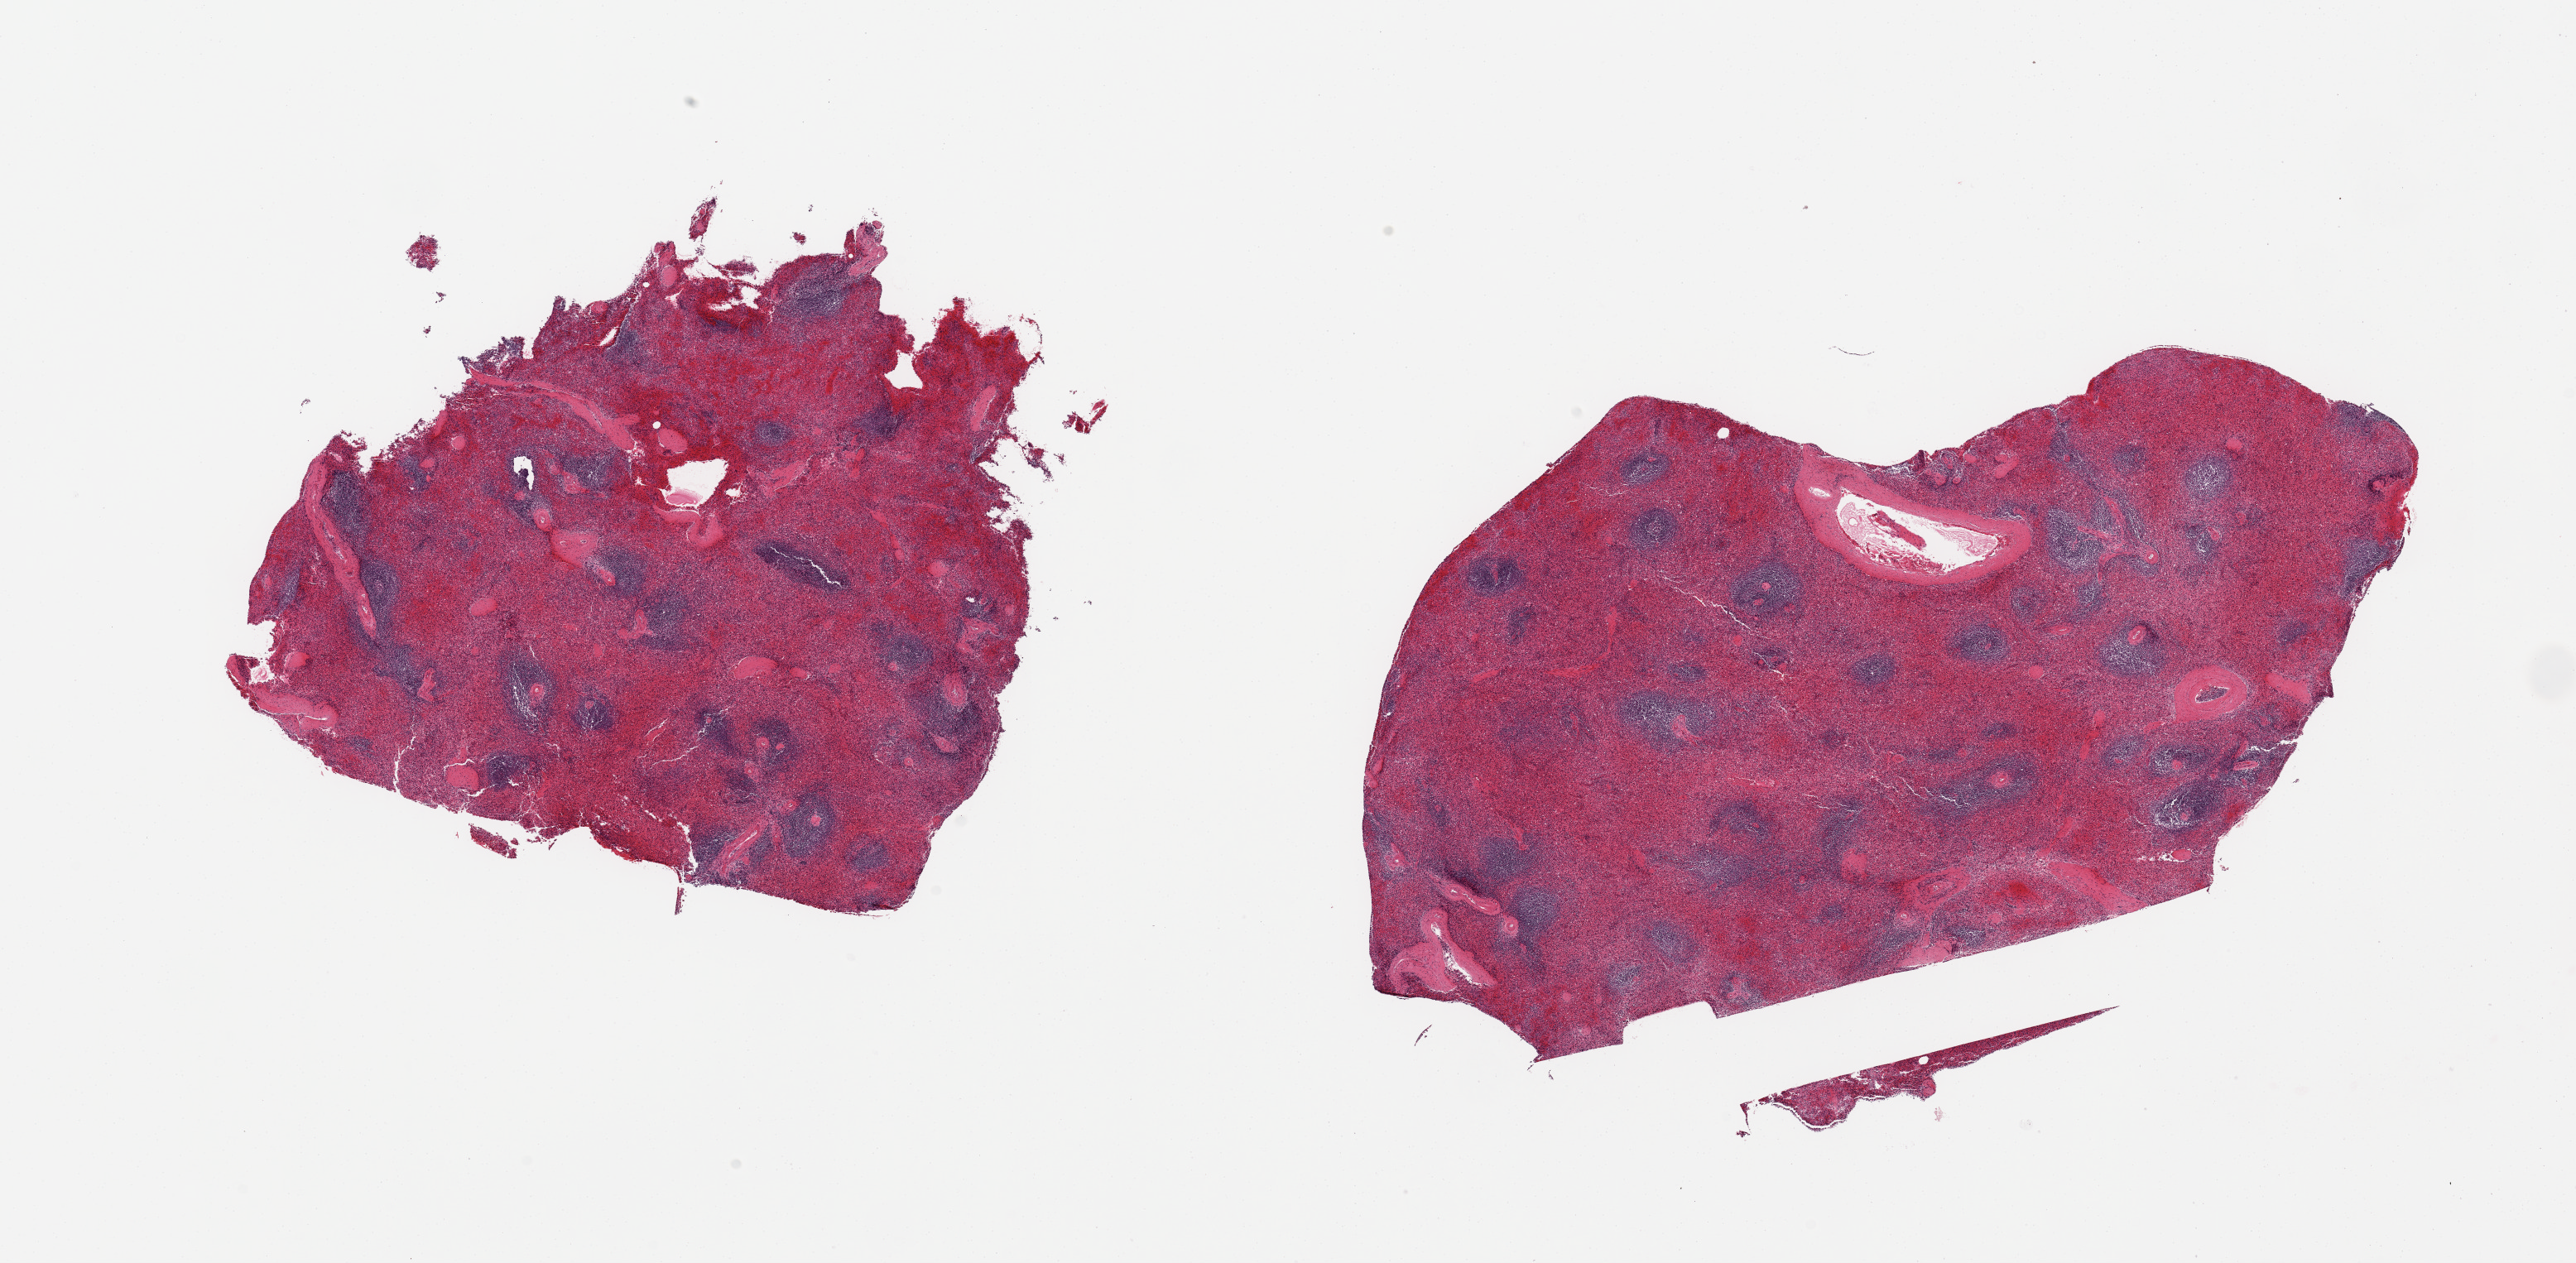
Hematoxylin and eosin (H&E) whole-slide image — a low-resolution overview of the entire scanned area, about 24.6 x 12.1 mm, PAXgene-fixed, paraffin-embedded tissue, section of spleen (target tissue), tissue donor sample. Donor: female.
- reviewer comment on this tissue sample: 2 pieces; moderate congestion